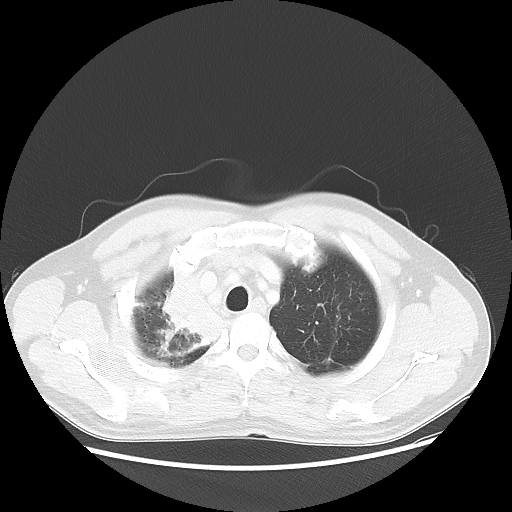
Chest CT, one axial slice; slice 46 of 56 in the series (ordered by position); lung window (W 1500 / L -600 HU); 512 × 512 image matrix. Male patient, age 60 years. Case-level facts recorded for this patient, not image findings: clinical TNM (as recorded): T2a N1 M0.
Structures marked on this image (bounding box drawn by a radiologist):
- lung tumour (recorded histology: squamous cell carcinoma): box from (x=142, y=254) to (x=232, y=380) px